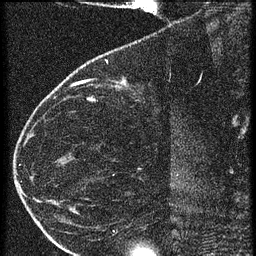
Breast MRI (dynamic contrast-enhanced), one sagittal slice; slice 18 of 60 in the series (ordered by position); 3 images stored at this slice position (order not interpretable as contrast timing); 1.5 T; TE 4.2 ms, TR 20.4 ms; 1.5 mm slice thickness; 256 × 256 image matrix, field of view 180 × 180 mm. Patient: female, 35 years. From the clinical record (not read from this slice): setting: breast cancer imaged before/during neoadjuvant chemotherapy; receptor status: HR-positive, HER2-negative.
Annotated regions visible in this slice (semi-automatically segmented with operator editing):
- analysis volume of interest (the breast-tissue region the enhancement analysis was run in; not a lesion): box from (x=65, y=60) to (x=169, y=119) px
- tumour enhancement mask (voxels above the 90 % enhancement threshold inside the analysis volume of interest): (x=121, y=80)–(x=125, y=83)